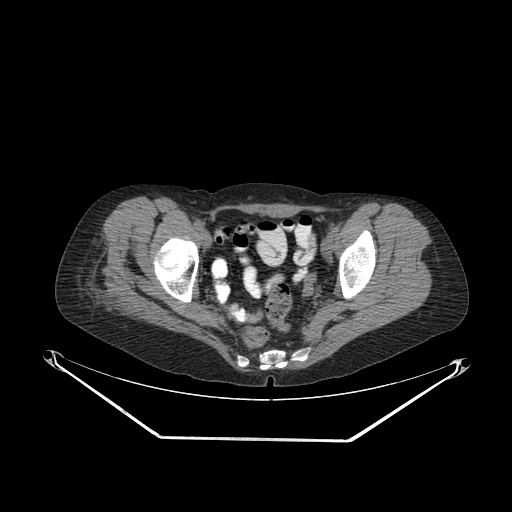
CT of an extremity soft-tissue mass (from a PET/CT study), one axial slice; slice 57 of 267 in the series (ordered by position); reconstruction kernel SOFT; 140 kVp; soft-tissue window (W 400 / L 40 HU); 3.75 mm slice thickness; 512 × 512 image matrix, field of view 500 × 500 mm. Female patient. From the clinical record (not read from this slice): histological type: epithelioid sarcoma with vascular differentiation; site of the primary tumour: right buttock.
Annotated regions visible in this slice (expert contour drawn on MRI and transferred to this co-registered scan by the dataset authors):
- gross tumour volume (mass): box from (x=84, y=283) to (x=122, y=291) px